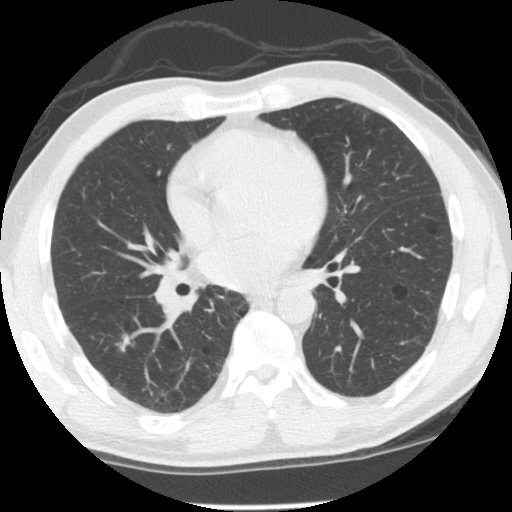
Axial slice from a low-dose chest CT screening exam. First (baseline) screen. Lung window (W 1500 / L -600 HU). Standard (soft-tissue) reconstruction kernel (STANDARD). Slice 55 of 125 in the series. 512 × 512 image matrix, field of view 330 × 330 mm. Male participant, aged 60 years at enrolment. Former smoker at enrolment.
Expert reader's lesion annotation, box from (x=92, y=322) to (x=143, y=368) px. Screening reader's record for this exam (one nodule recorded; not confirmed to be the boxed lesion): non-calcified nodule or mass ≥4 mm, right lower lobe, 9 × 7 mm, spiculated (stellate) margins. Later outcome: lung cancer diagnosed 534 days after this screen (after the second annual screen) — adenocarcinoma, NOS, right lower lobe, stage IA (AJCC 6th edition), 18 mm at pathology.